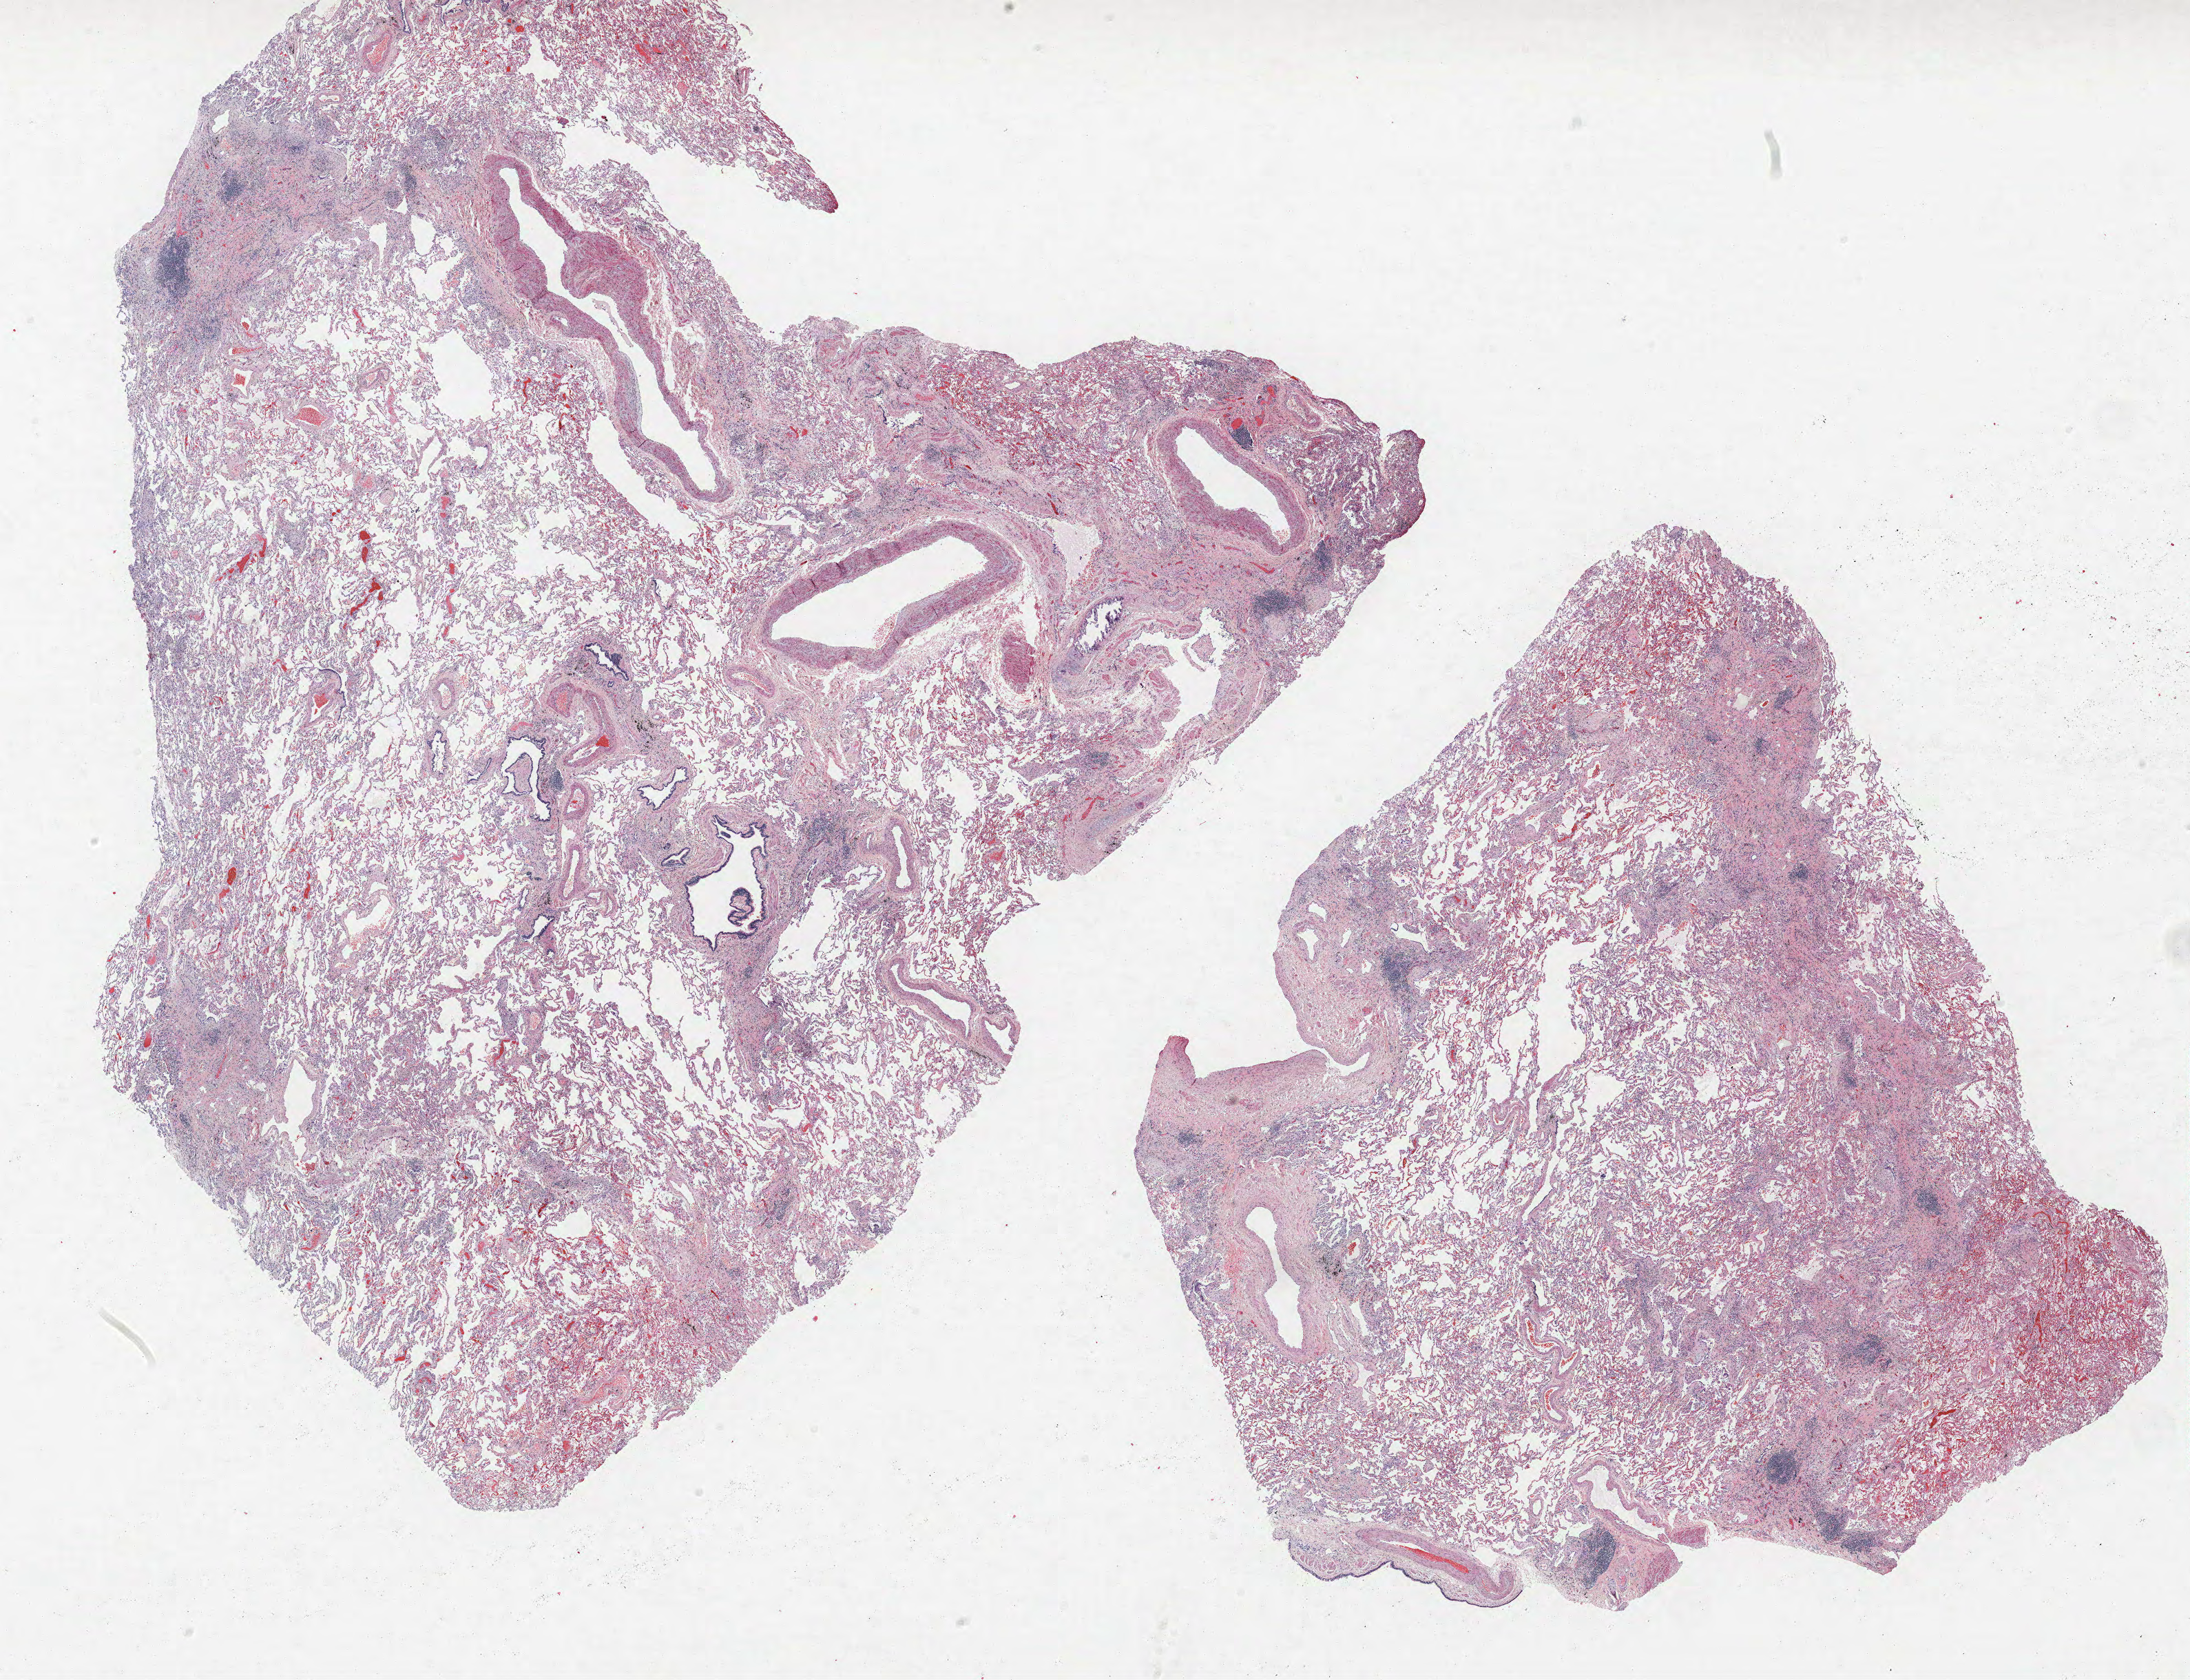
Whole-slide histology image, H&E — whole scanned area (about 25.4 x 19.5 mm) shown as a low-resolution overview. FFPE section. Lung tissue. Male patient, aged 68 at enrolment. Former smoker at enrolment.
Participant's lung-cancer diagnosis: Squamous cell carcinoma, NOS (ICD-O-3 8070/3).